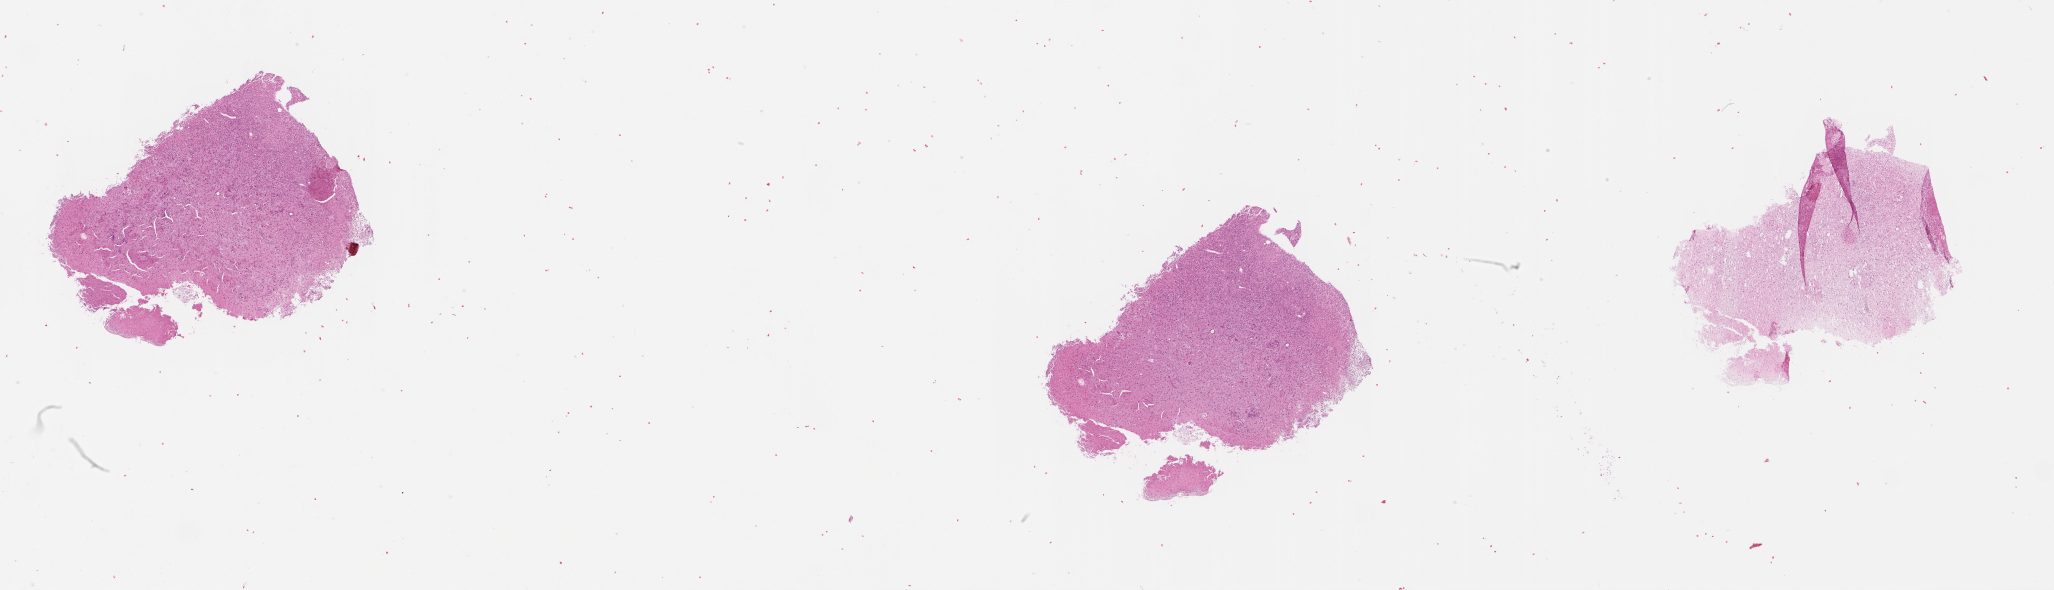
Whole-slide histology image, H&E, shown as a low-resolution overview of the whole scanned area (about 33.1 x 9.5 mm, slide scanned at 20x), tumour tissue sample, sampled site: brain. Male, 66 y/o. Composition of this section per pathologist review: tumour nuclei 60%, necrosis 5%.
Histologic diagnosis: Glioblastoma. Primary tumour site (as recorded): temporal lobe.